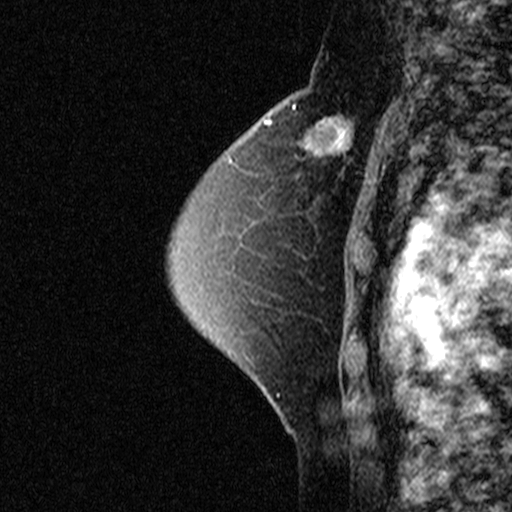
Breast MRI (dynamic contrast-enhanced), one sagittal slice; position 29 of 44 along the scan axis; dynamic contrast-enhanced study with each time point stored as its own series, time point 2 of 3 at this slice position (early post-contrast, ordered by acquisition time); 1.5 T; TE 4.5 ms, TR 11 ms; 512 × 512 image matrix, field of view 200 × 200 mm. Female patient, age 49 years. Case-level facts recorded for this patient, not image findings: setting: breast cancer imaged before/during neoadjuvant chemotherapy; receptor status: triple-negative.
Structures marked on this image (semi-automatic segmentation, software-assisted and operator-edited):
- analysis volume of interest (the breast-tissue region the enhancement analysis was run in; not a lesion): bounding box <276,94,369,181> (left, top, right, bottom; pixels)
- tumour enhancement mask (voxels above the 90 % enhancement threshold inside the analysis volume of interest): <293,104,354,156>